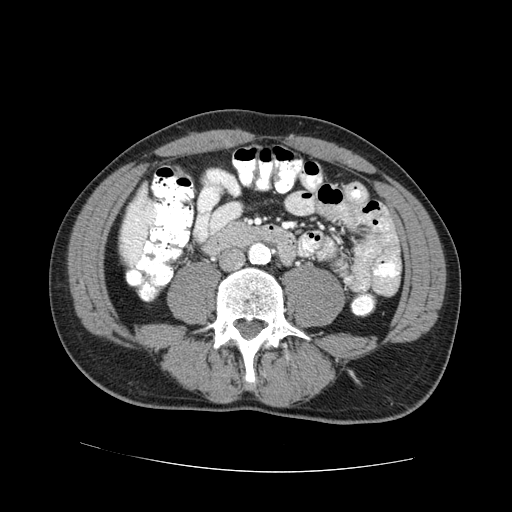
Contrast-enhanced abdominal CT (liver protocol), one axial slice. Position 5 of 73 along the scan axis. 100 kVp. One of 2 acquisitions stored at this slice position. Soft-tissue window (W 400 / L 40 HU). 2.5 mm slice thickness. 512 × 512 image matrix, field of view 380 × 380 mm. Case-level facts recorded for this patient, not image findings: diagnosis: hepatocellular carcinoma (patient treated with transarterial chemoembolisation; whether this scan precedes or follows treatment is not stated here); TNM stage (as recorded): Stage-IVA; Child-Pugh class: A.
Outlined on this slice (semi-automatically segmented with operator editing):
- liver parenchyma outside the tumour (the mass and vessels are separate outlines, so this box may not span the whole liver): bounding box [x1, y1, x2, y2] px = [120, 190, 152, 262]